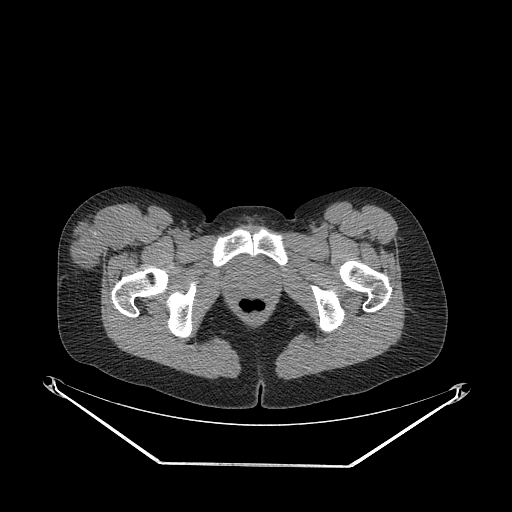
CT of an extremity soft-tissue mass (from a PET/CT study), one axial slice. Slice 60 of 267 in the series (ordered by position). 140 kVp. Soft-tissue window (W 400 / L 40 HU). 3.75 mm slice thickness. 512 × 512 image matrix, field of view 500 × 500 mm. Female patient. From the clinical record (not read from this slice): histological type: synovial sarcoma; grade: intermediate; site of the primary tumour: right thigh.
Structures marked on this image (expert contour drawn on MRI and transferred to this co-registered scan by the dataset authors):
- gross tumour volume including surrounding oedema: bounding box [x1, y1, x2, y2] px = [69, 212, 122, 270]
- gross tumour volume (mass): [69, 212, 122, 270]